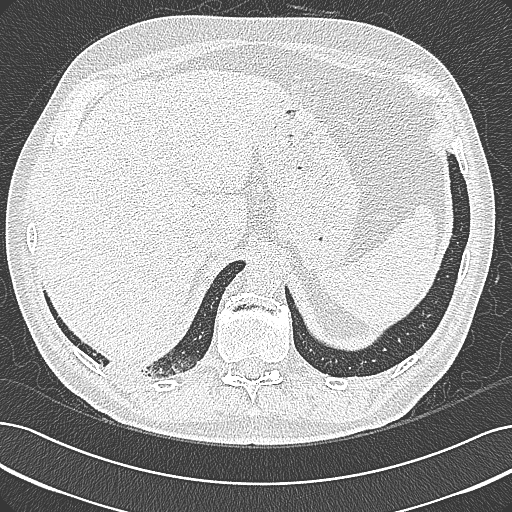
Axial slice from a low-dose chest CT screening exam, first (baseline) screen, lung window (W 1500 / L -600 HU), lung (sharp) reconstruction kernel (B80f), 120 kVp, slice 266 of 355 in the series, 512 × 512 image matrix. Male, age 68 years at enrolment. Former smoker at enrolment.
Expert-annotated lung lesion, bounding box (x1, y1, x2, y2) in pixels: (92, 335, 198, 395). Screening reader's record for this exam: no non-calcified nodule ≥4 mm recorded. Lung cancer was diagnosed 154 days after this screen: mucinous adenocarcinoma, right lower lobe, well differentiated (G1), stage IB (AJCC 6th edition), 50 mm at pathology.